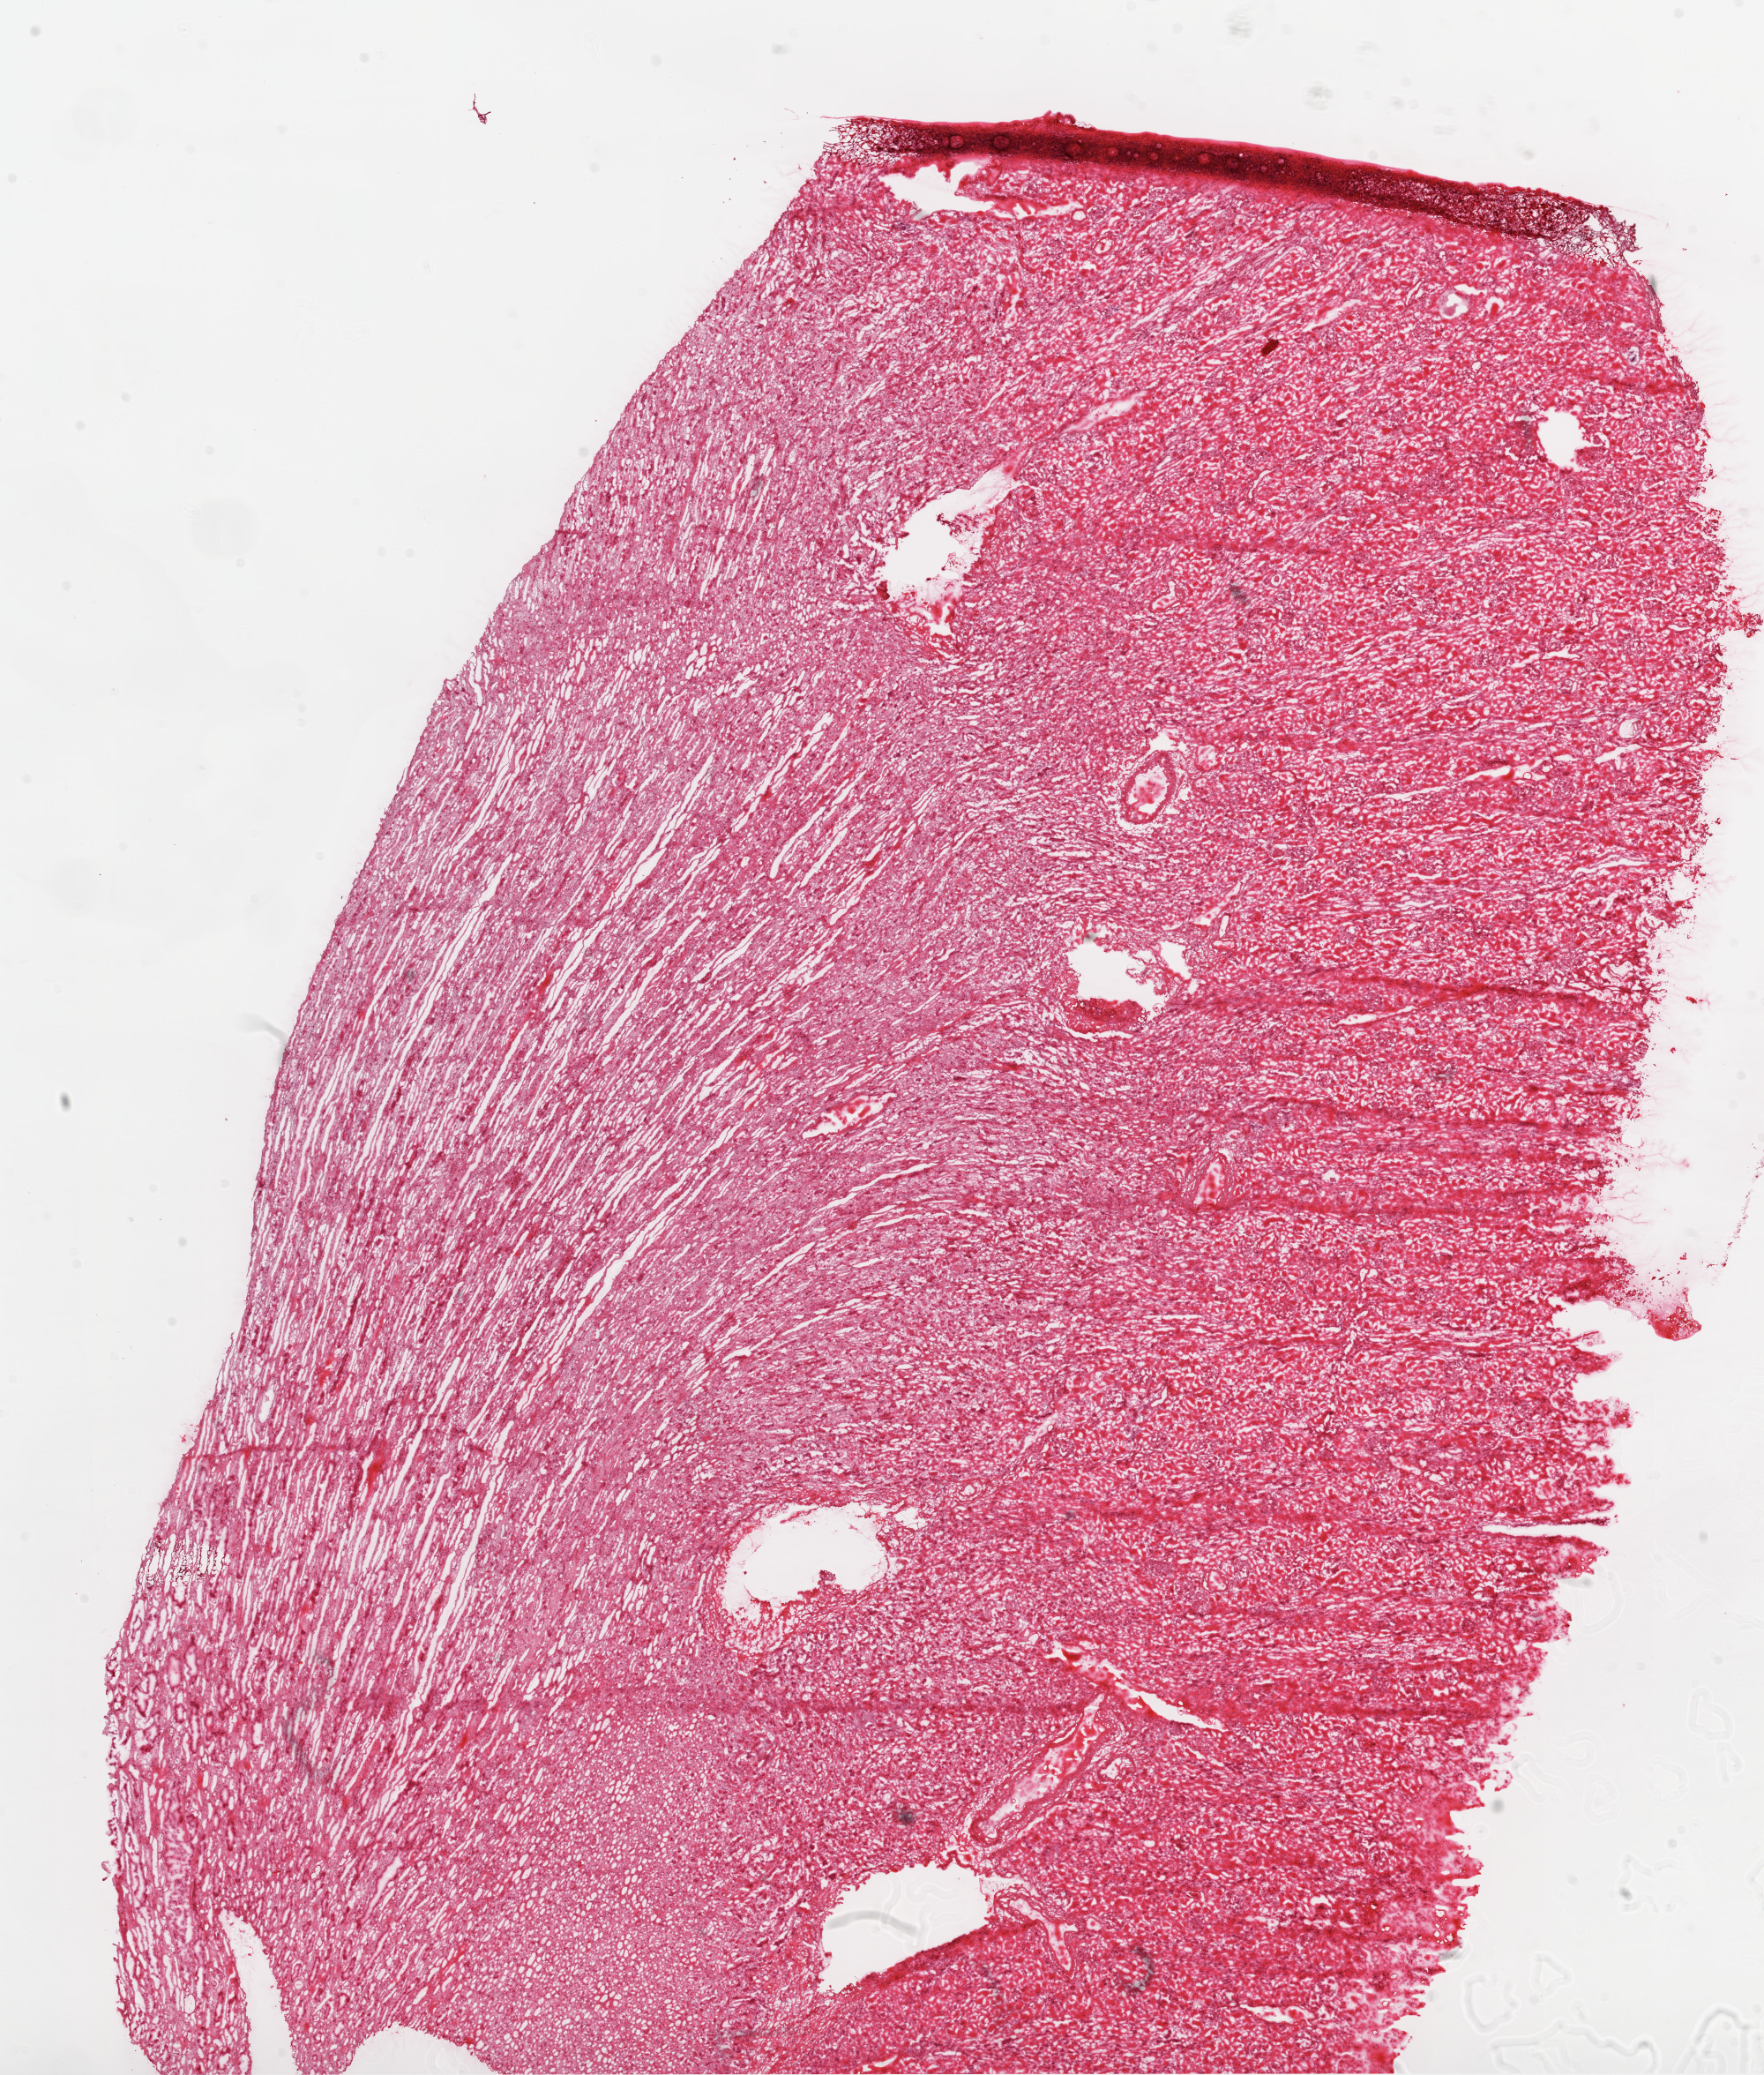
H&E-stained whole-slide image, low-resolution overview of the scanned area, about 16.0 x 18.9 mm (from a 20x scan), frozen section, sample: solid tissue normal (non-tumour tissue), kidney. Patient: female, age at initial diagnosis 65 years.
This section: solid tissue normal (non-tumour) sample from the same patient. Patient diagnosis: Clear cell adenocarcinoma, NOS.